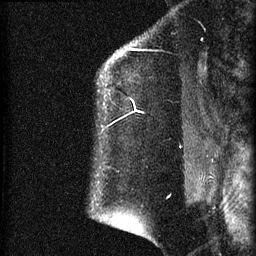
Breast MRI (dynamic contrast-enhanced), one sagittal slice; dynamic contrast-enhanced series, image 2 of 4 at this slice position (ordered by acquisition); 1.5 T; TE 4.2 ms, TR 22.7 ms; 1.5 mm slice thickness; 256 × 256 image matrix. Patient: female, 35 years. Case-level facts recorded for this patient, not image findings: setting: breast cancer imaged before/during neoadjuvant chemotherapy; receptor status: HR-positive, HER2-negative.
Outlined on this slice (semi-automatically segmented with operator editing):
- analysis volume of interest (the breast-tissue region the enhancement analysis was run in; not a lesion): bounding box (x1, y1, x2, y2) in pixels: (70, 27, 199, 112)
- tumour enhancement mask (voxels above the 90 % enhancement threshold inside the analysis volume of interest): (131, 99, 141, 112)